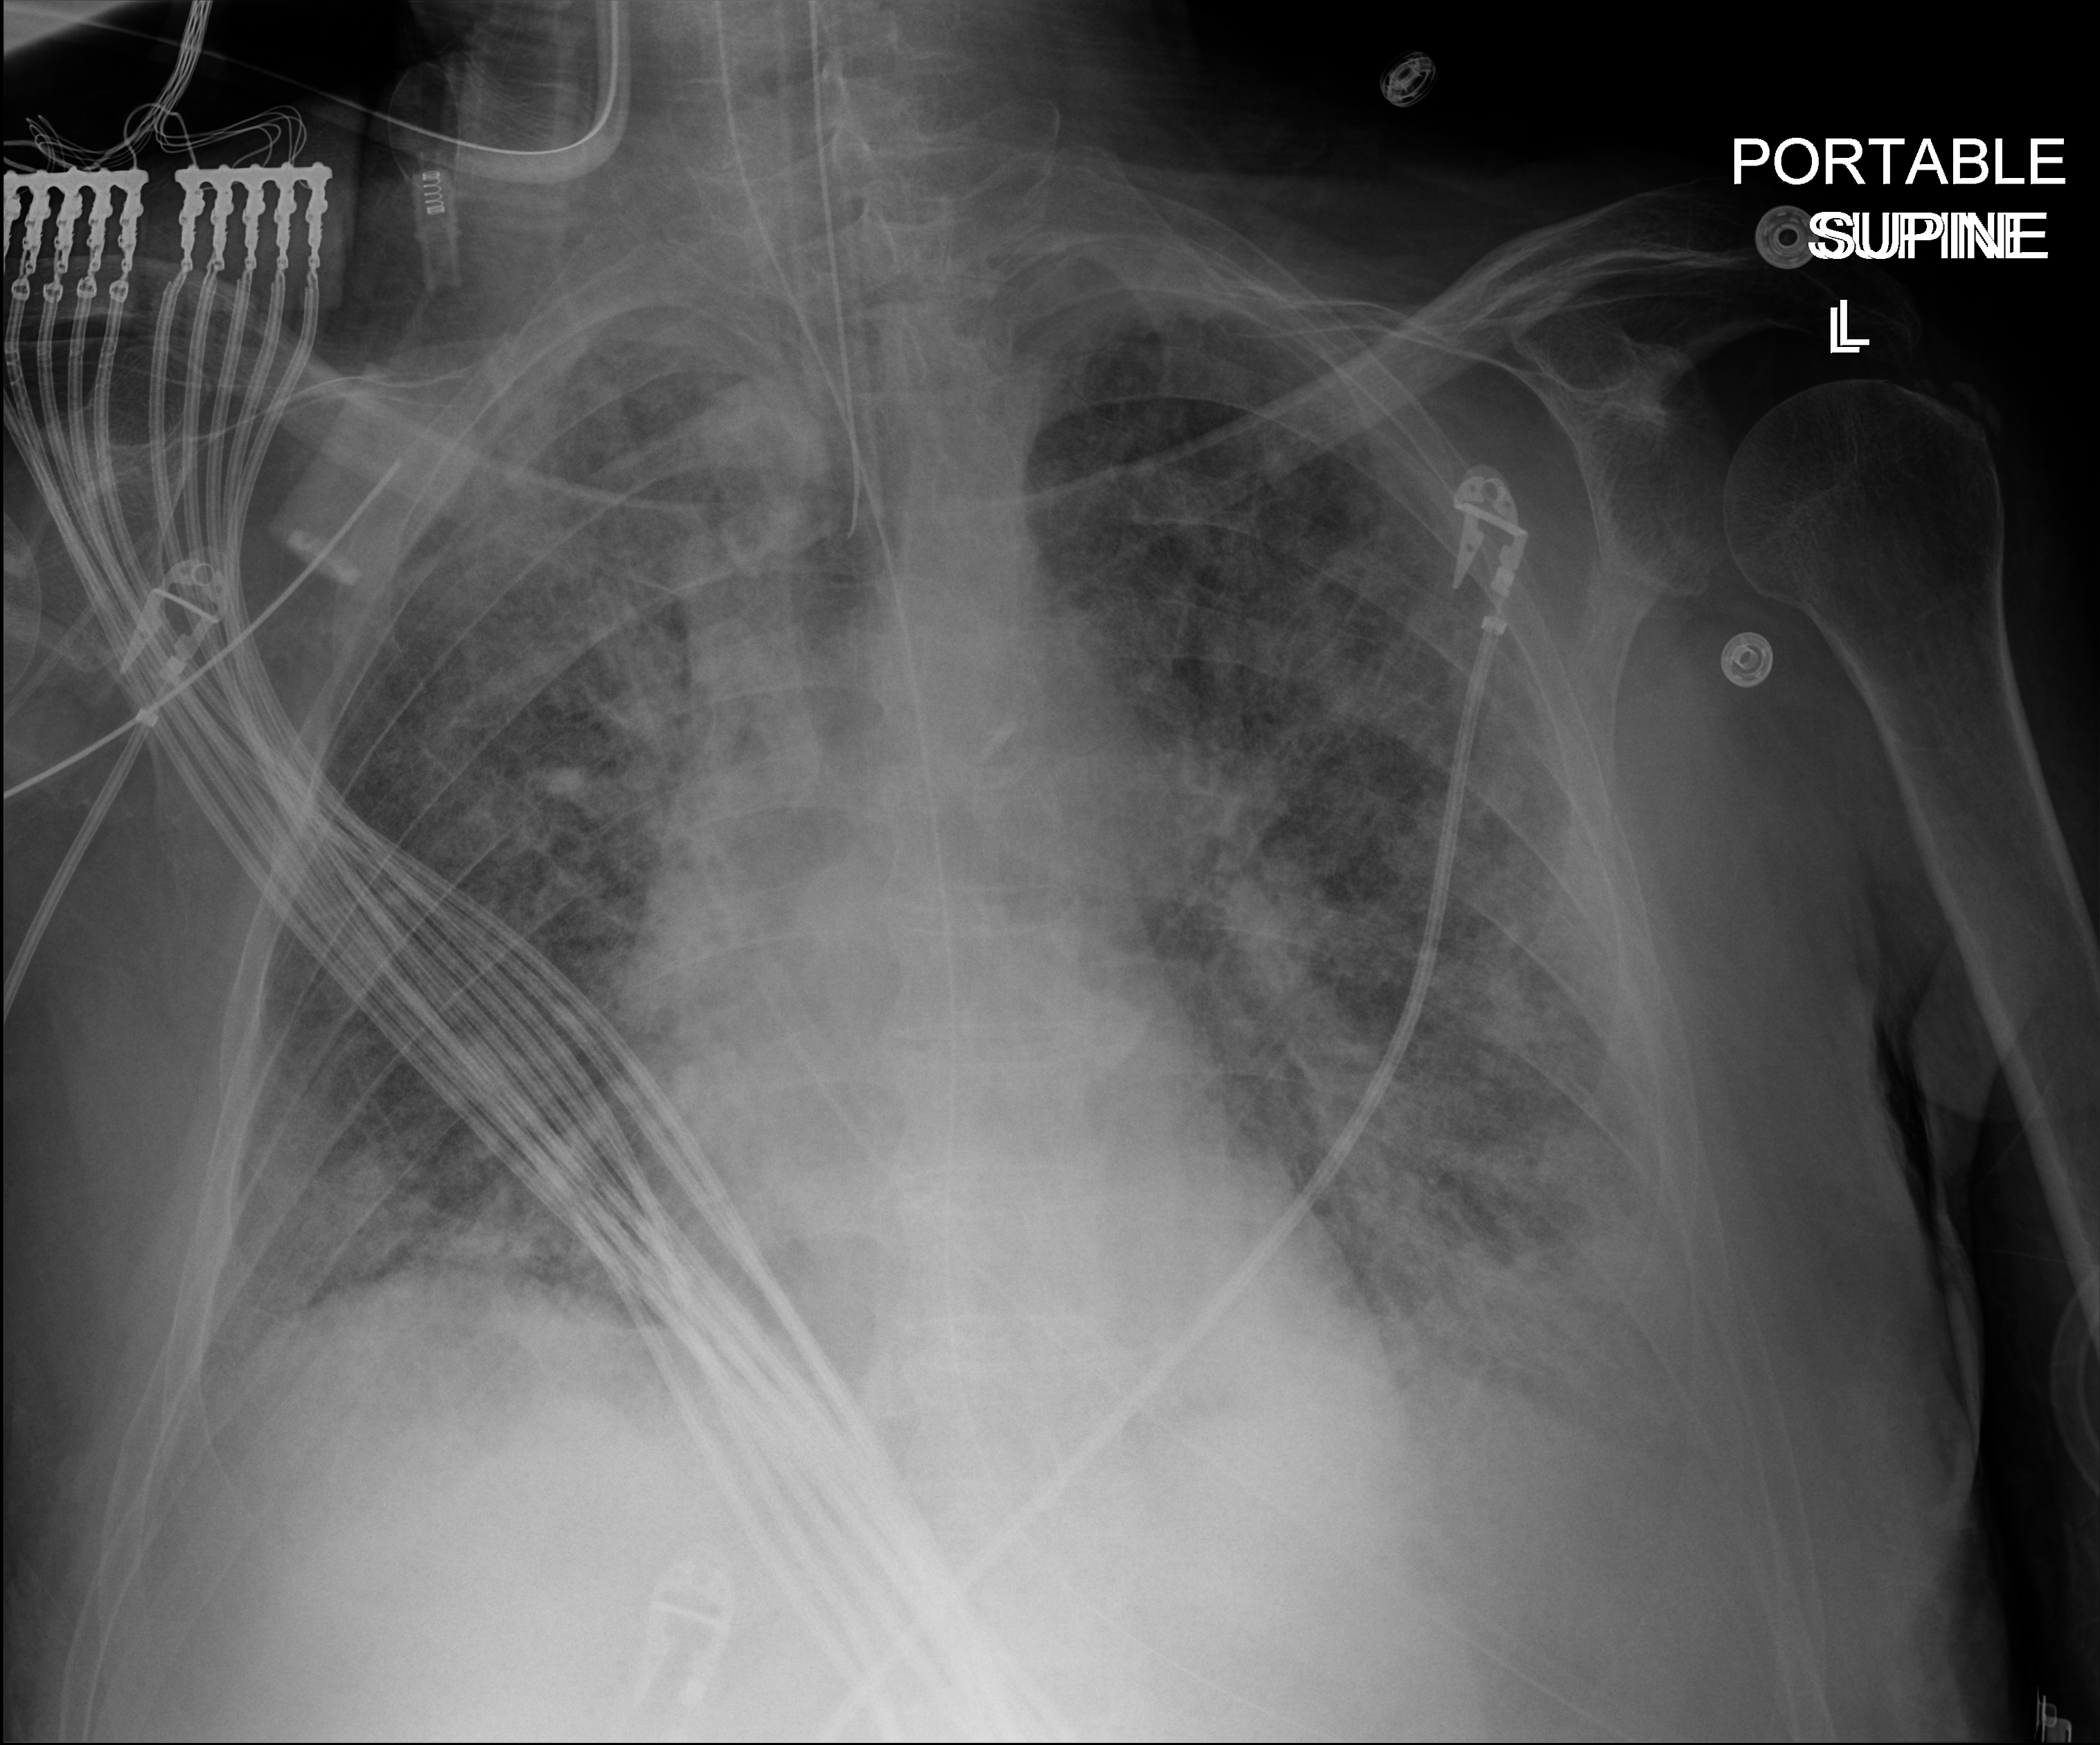
Chest radiograph (digital radiography), anteroposterior (AP) projection. Male patient hospitalised with COVID-19, age 60–74 years.
From the hospital-stay record, not from the radiograph (when in the stay this image was taken is not recorded):
- chronic kidney disease (admission record): no
- admitted to intensive care during this hospital stay: yes
- mechanically ventilated during this hospital stay: yes